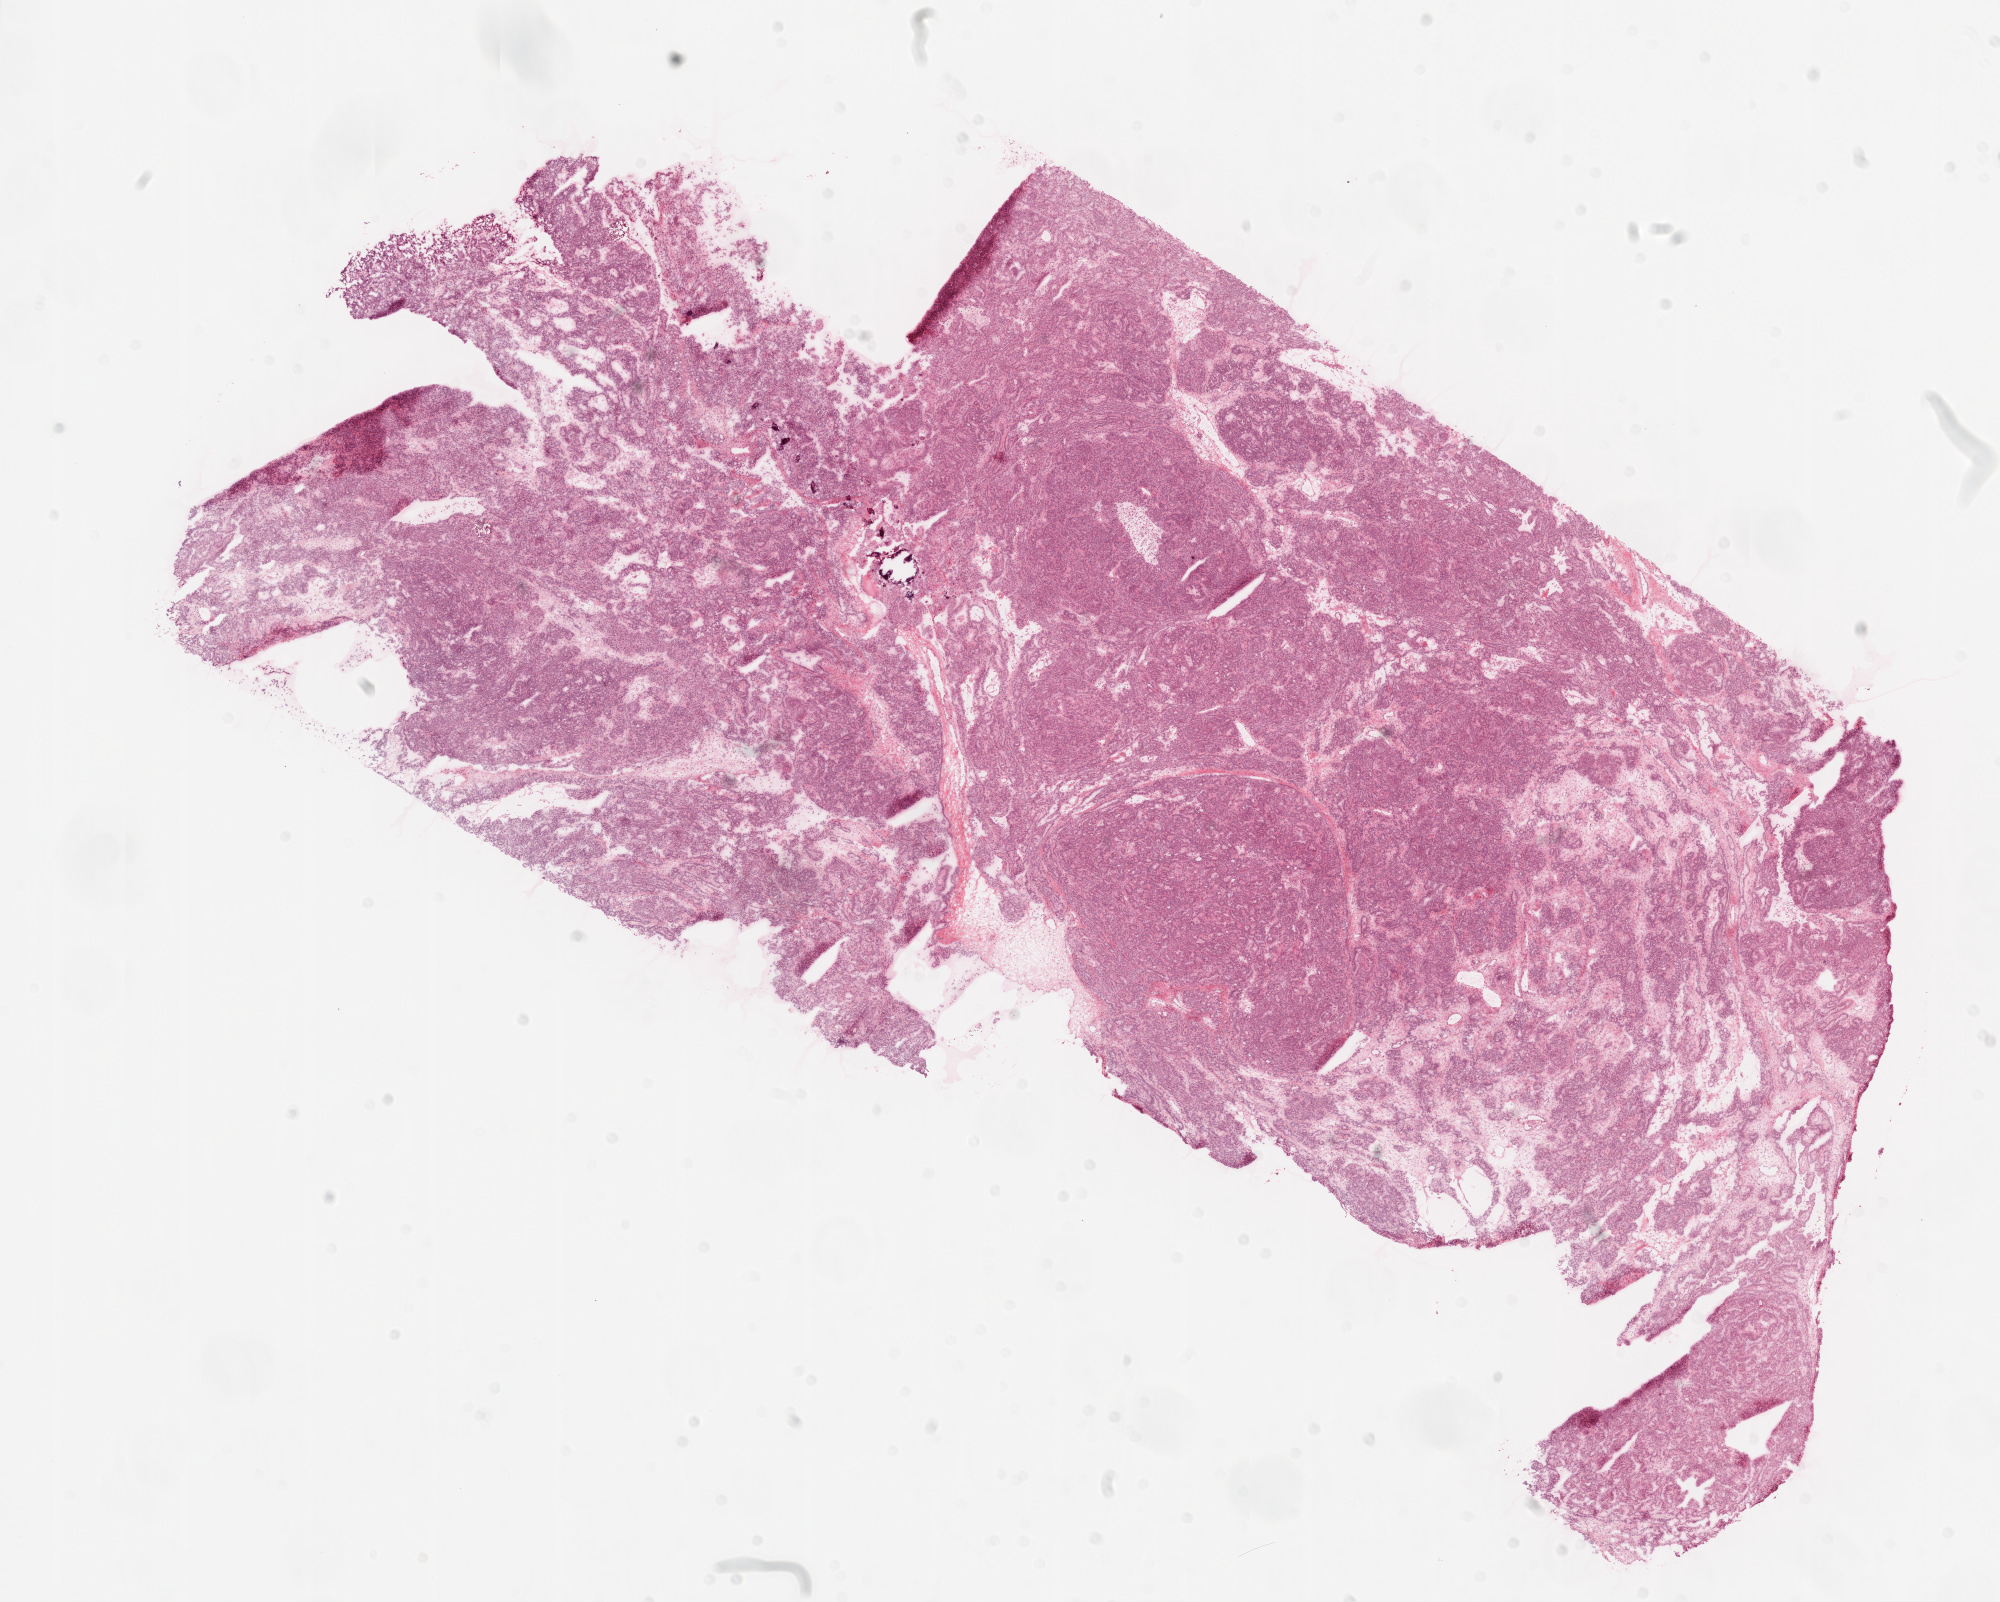
Digitized Hematoxylin and eosin (H&E) stained tissue section (whole slide) — low-resolution overview of the scanned area, about 16.0 x 12.9 mm; frozen section from the top of the tissue portion; sample: primary tumour, ovary. Female, age 50 years at initial diagnosis. Histologic grade: G2 (moderately differentiated). Pathologist review of this section (percent, as recorded): tumour cells 90%, tumour nuclei 90%, normal cells 0%, stromal cells 10%, necrosis 0%.
Histologic diagnosis: Serous cystadenocarcinoma, NOS. FIGO stage: IV.